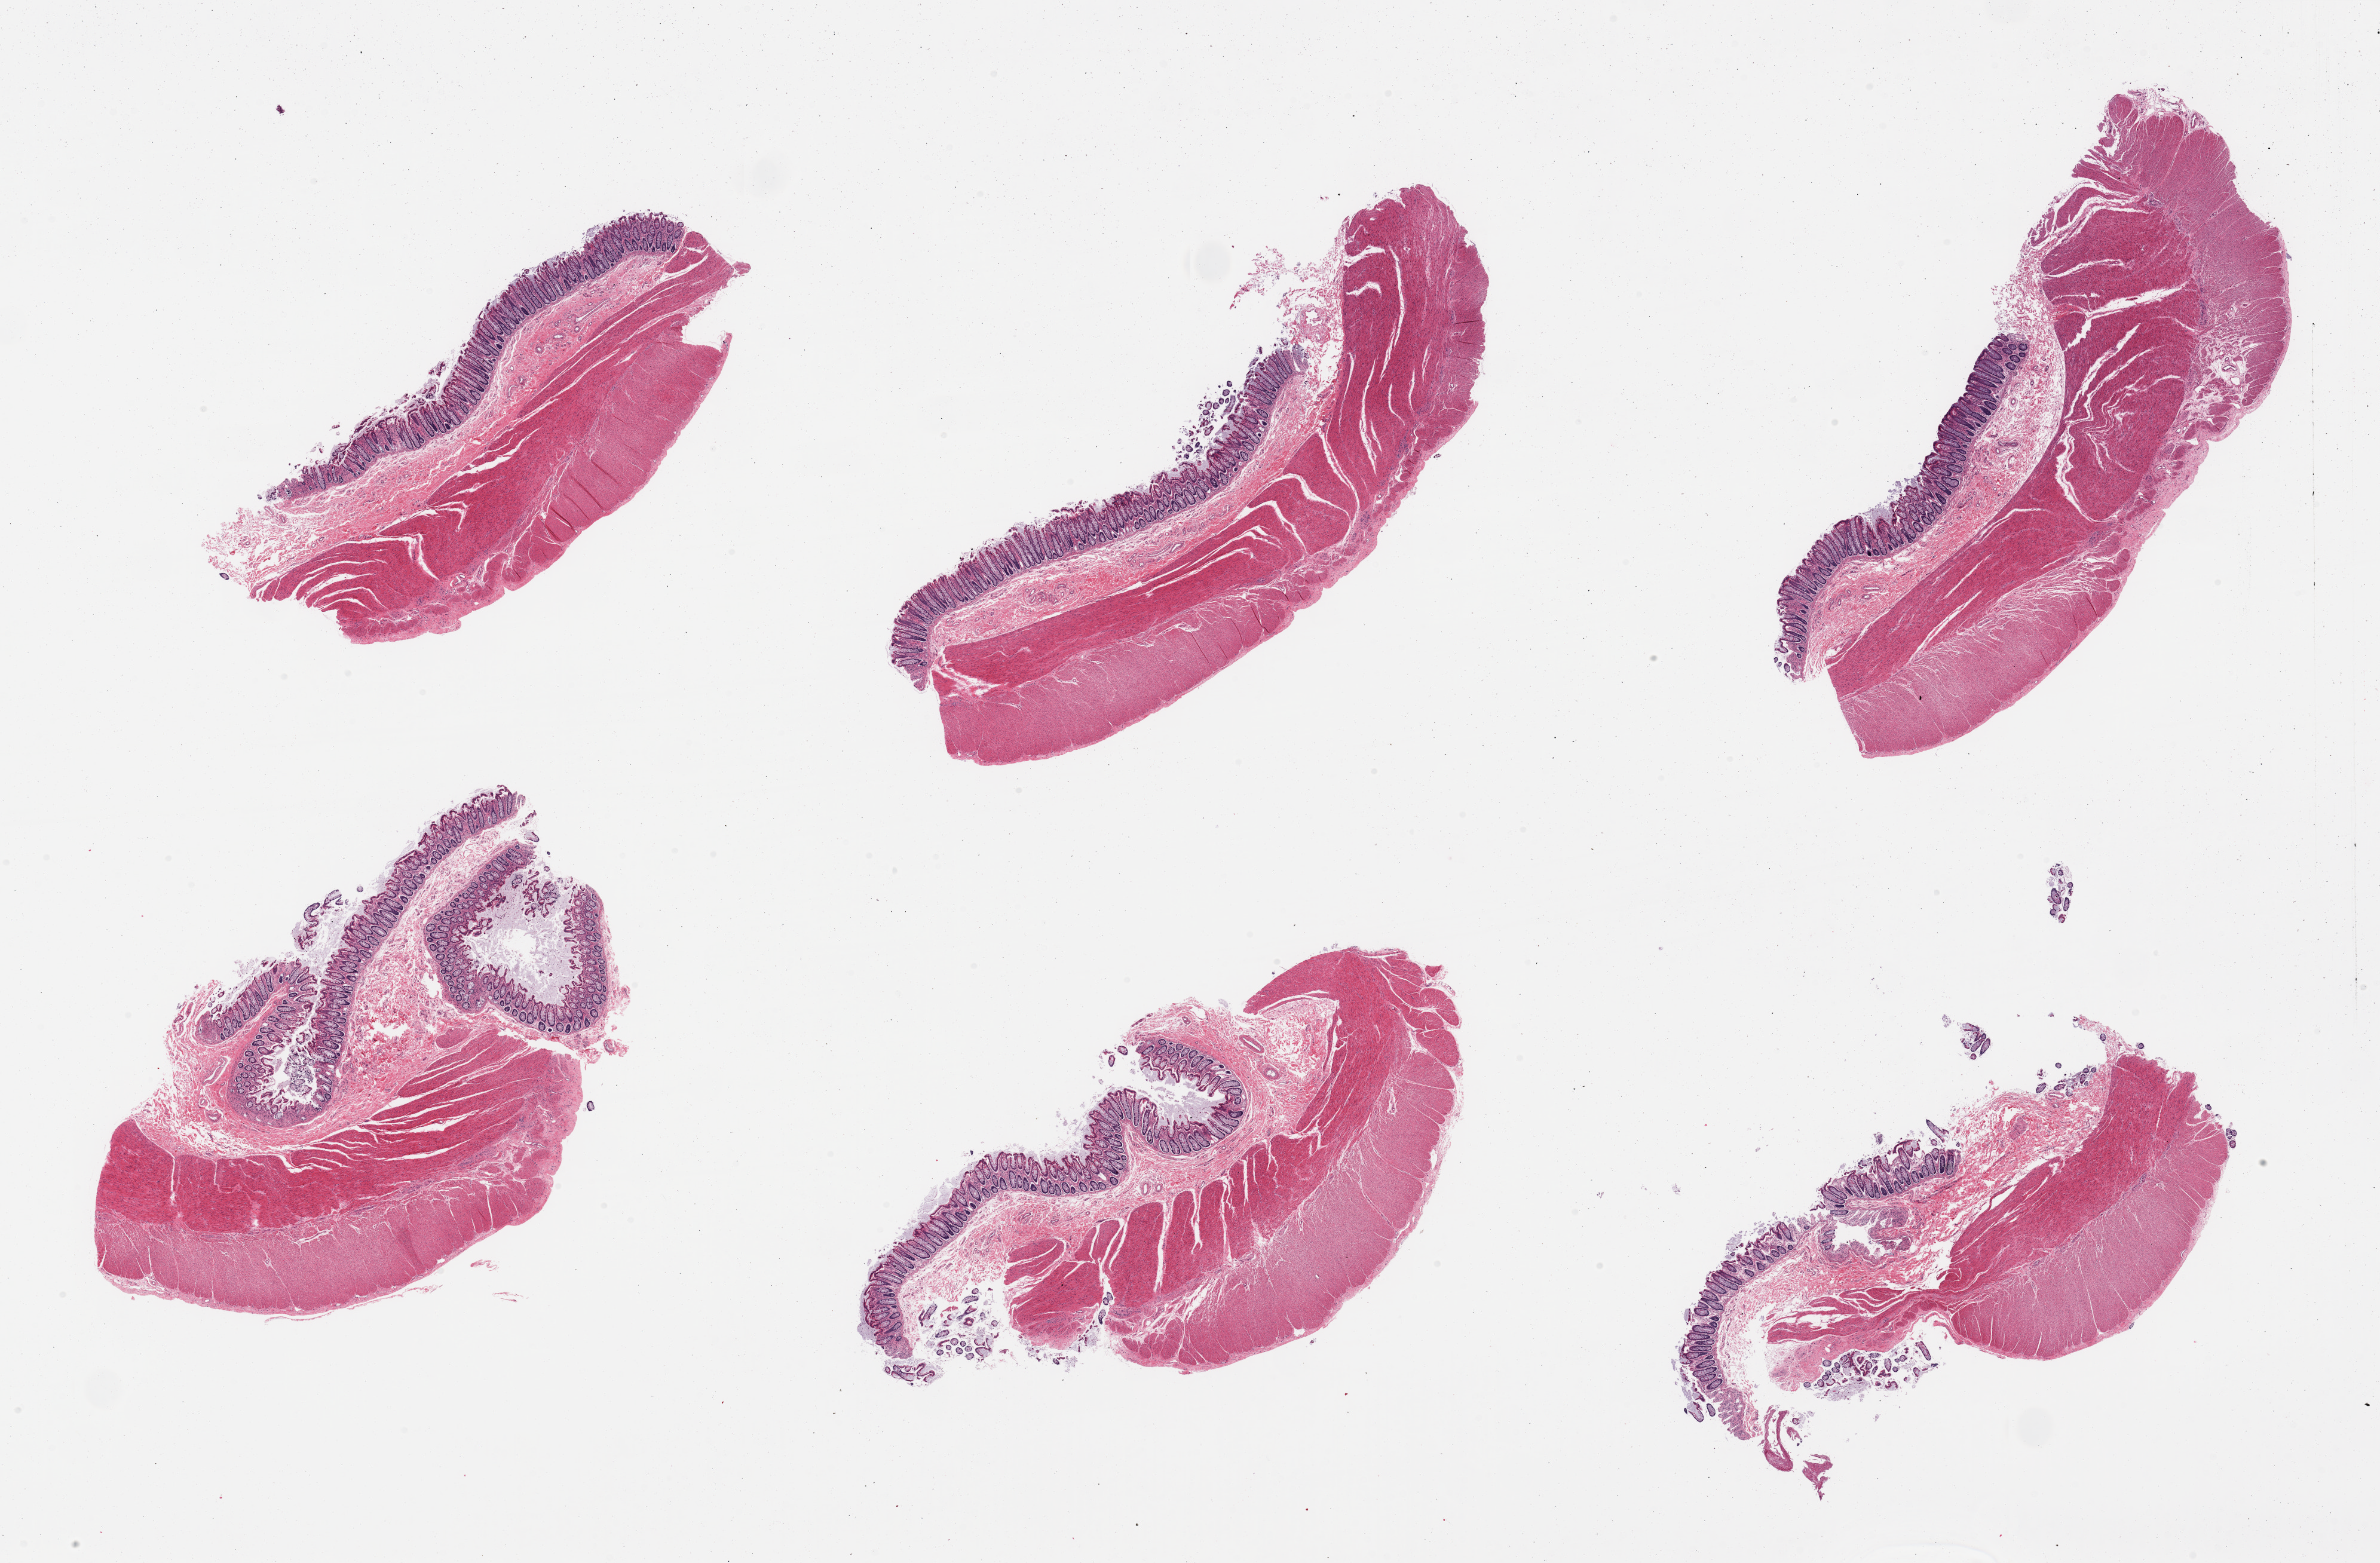
Whole-slide image, hematoxylin and eosin (H&E) stain — whole scanned area (about 31.5 x 20.7 mm, acquisition: 20x scan) shown as a low-resolution overview; PAXgene-fixed paraffin-embedded (PFPE) section; target tissue: ileum; tissue donor sample. Donor sex: male.
• review note (as recorded): 6 pieces; full thickness of colon sampled, NOT ileum